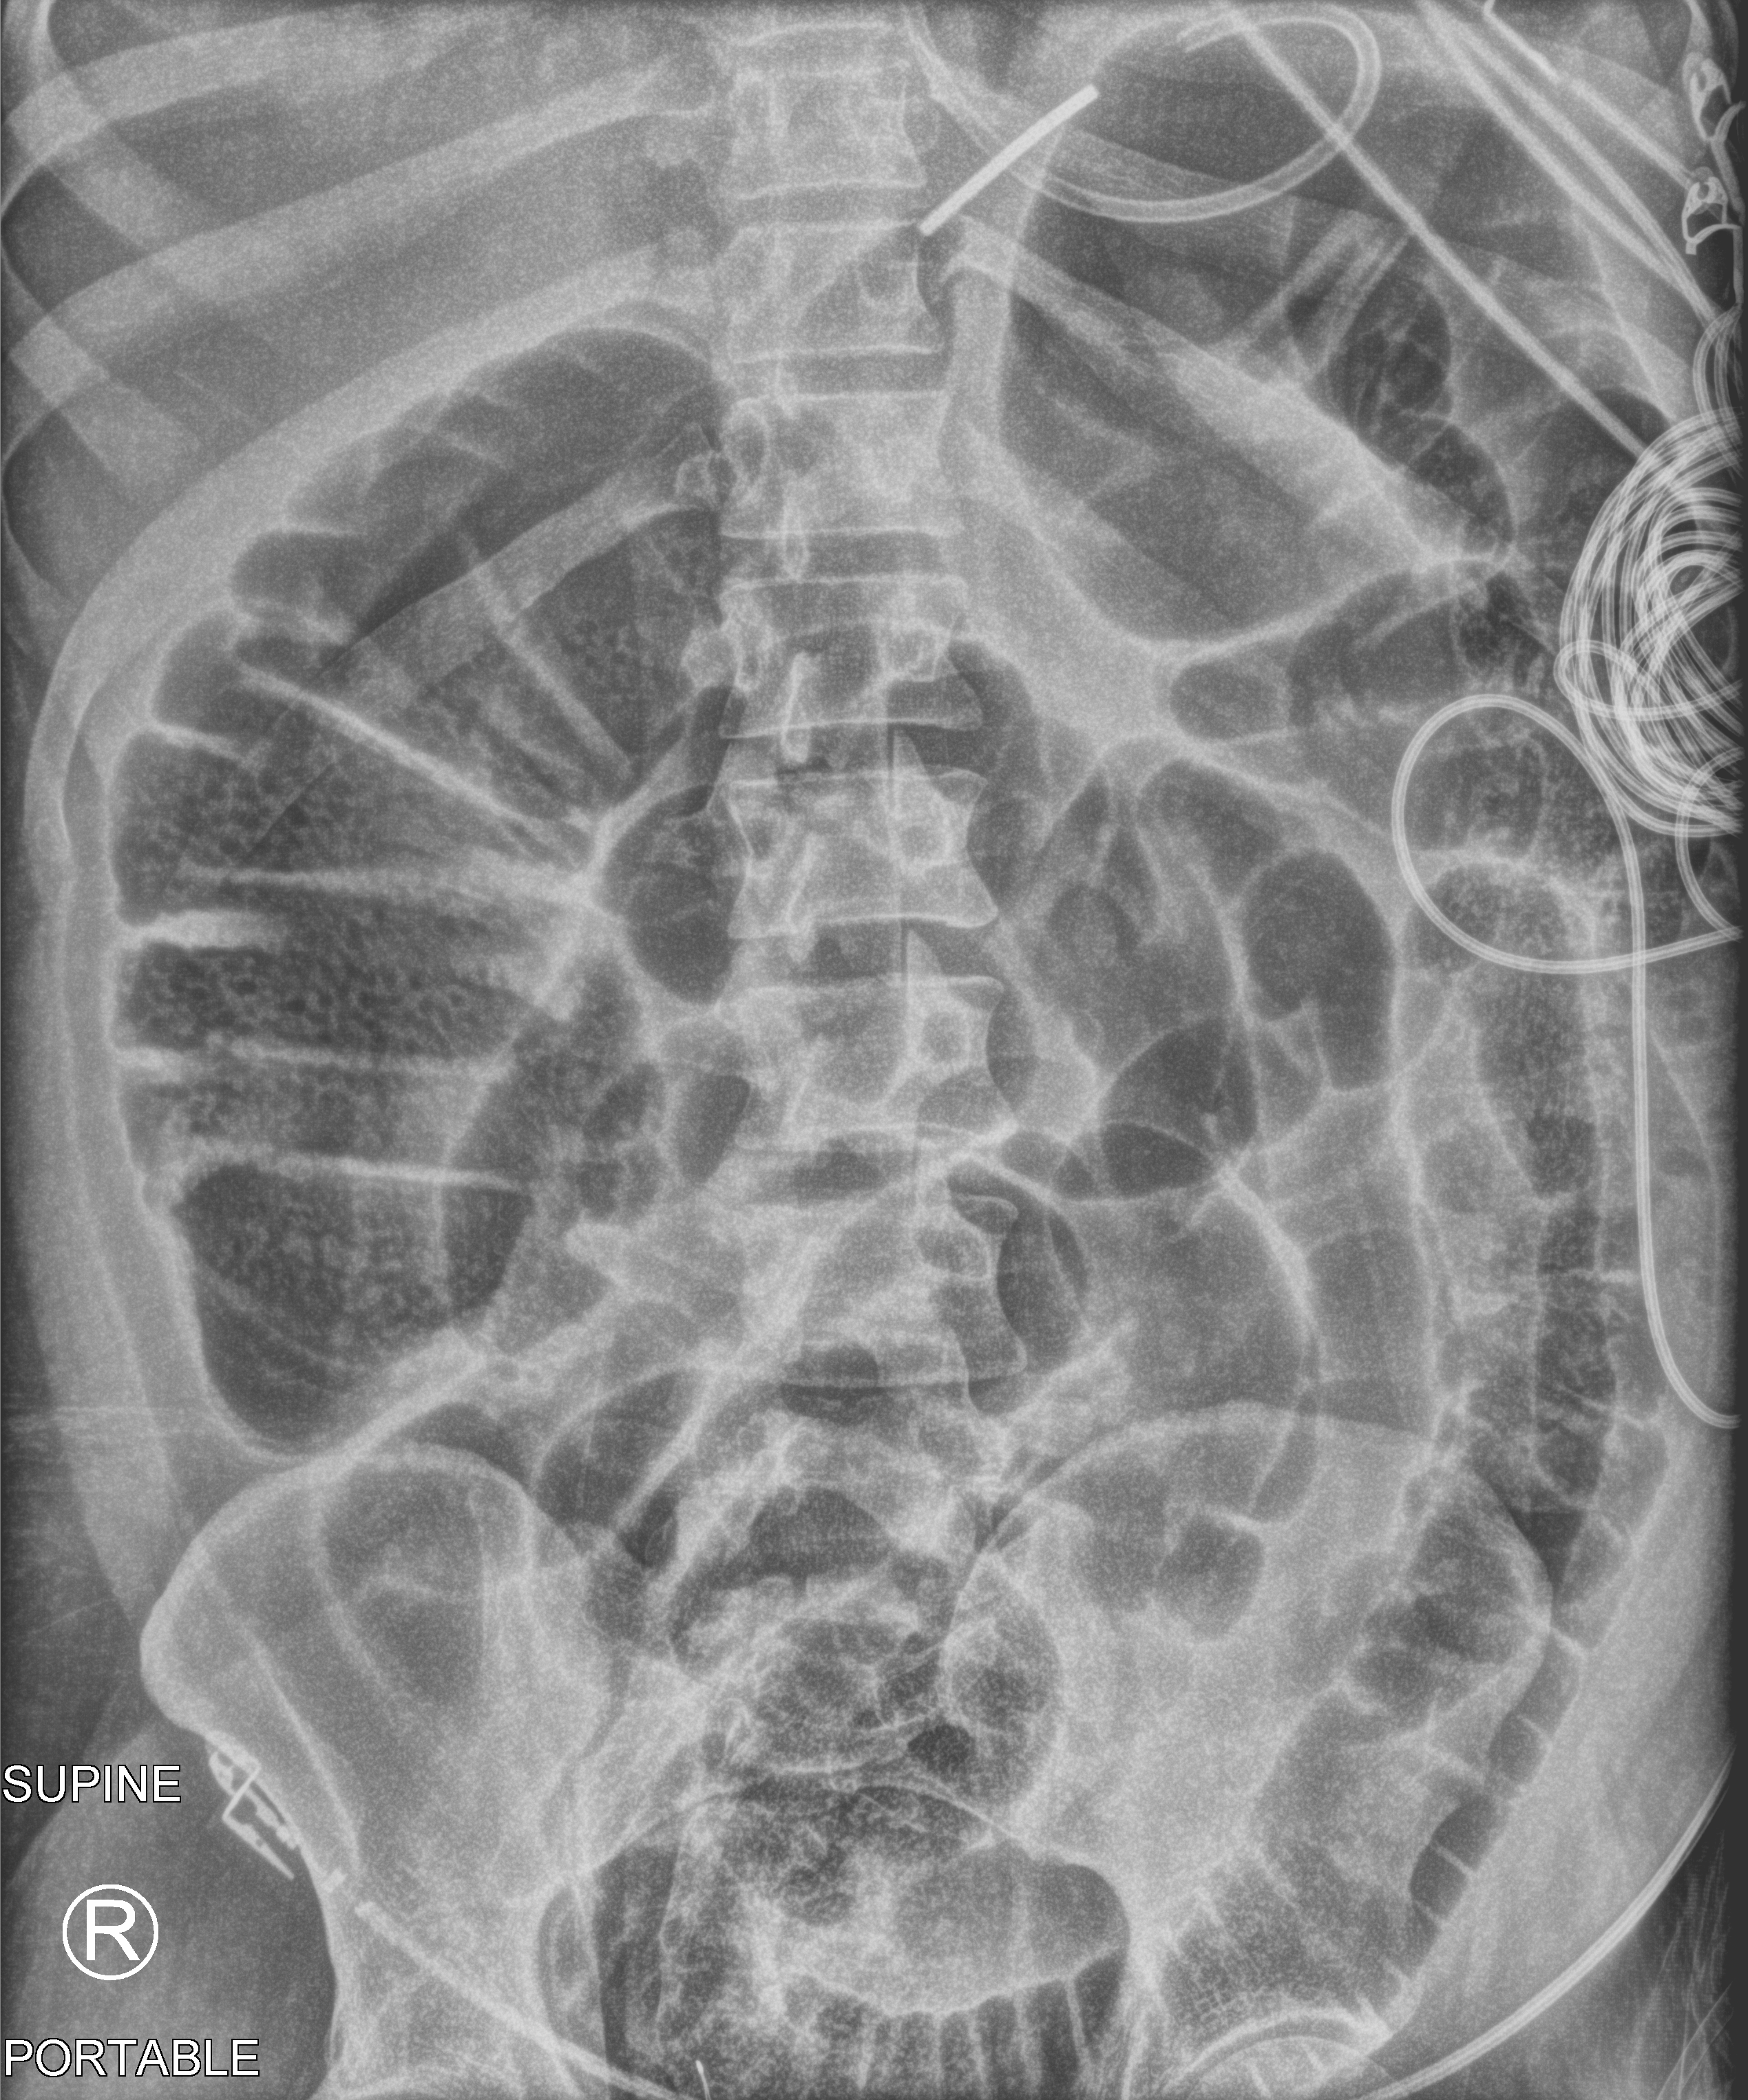
Abdomen X-ray (portable); anteroposterior (AP) projection. Male patient hospitalised with COVID-19, age 18–59 years.
Admission-level facts for this patient (not findings on this image; timing relative to this image not recorded): admitted to intensive care during this hospital stay: no.